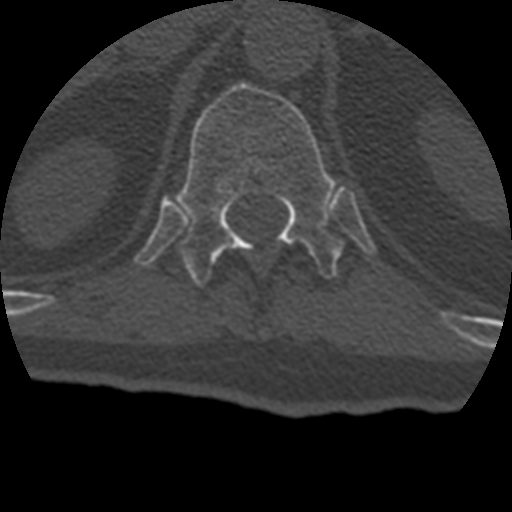
CT including the spine, one axial slice; position 178 of 399 along the scan axis; 120 kVp; bone window (W 1800 / L 400 HU); 512 × 512 image matrix. Patient age 69 years. Case-level facts recorded for this patient, not image findings: primary cancer: prostate.
Structures marked on this image (semi-automatically segmented with operator editing):
- T12 vertebra: box from (x=177, y=83) to (x=344, y=286) px